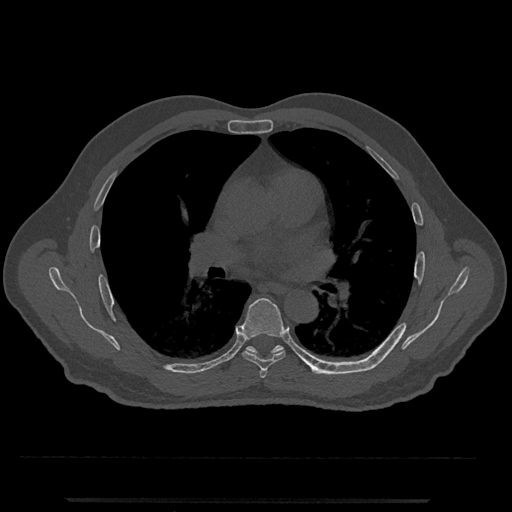
CT including the spine, one axial slice. Position 724 of 797 along the scan axis. Reconstruction kernel Br40s/3. 120 kVp. Bone window (W 1800 / L 400 HU). 0.5 mm slice thickness. 512 × 512 image matrix, field of view 419 × 419 mm. Patient: male, 63 years. Case-level facts recorded for this patient, not image findings: primary cancer: prostate.
Structures marked on this image (semi-automatically segmented with operator editing):
- T5 vertebra: box from (x=260, y=370) to (x=267, y=378) px
- T6 vertebra: (x=239, y=298)–(x=286, y=371)
- T7 vertebra: (x=246, y=345)–(x=330, y=375)